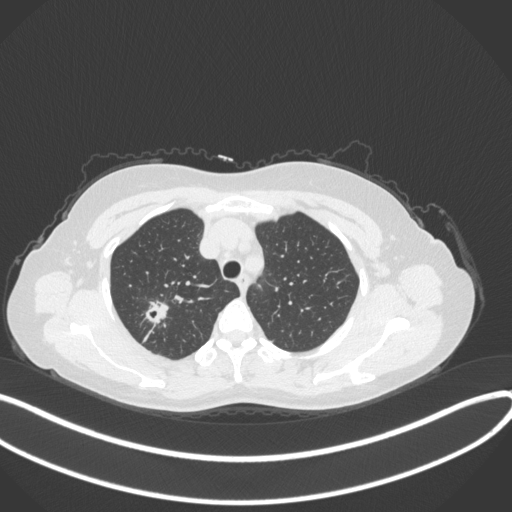
Chest CT, one axial slice. Position 290 of 342 along the scan axis. Reconstruction kernel B31f. Lung window (W 1500 / L -600 HU). 1 mm slice thickness. 512 × 512 image matrix, field of view 400 × 400 mm. Female patient, age 50 years. From the clinical record (not read from this slice): clinical TNM (as recorded): T1c N0 M0.
Outlined on this slice (rectangle marked by the reading radiologist):
- lung tumour (recorded histology: adenocarcinoma): bounding box [x1, y1, x2, y2] px = [141, 294, 172, 327]